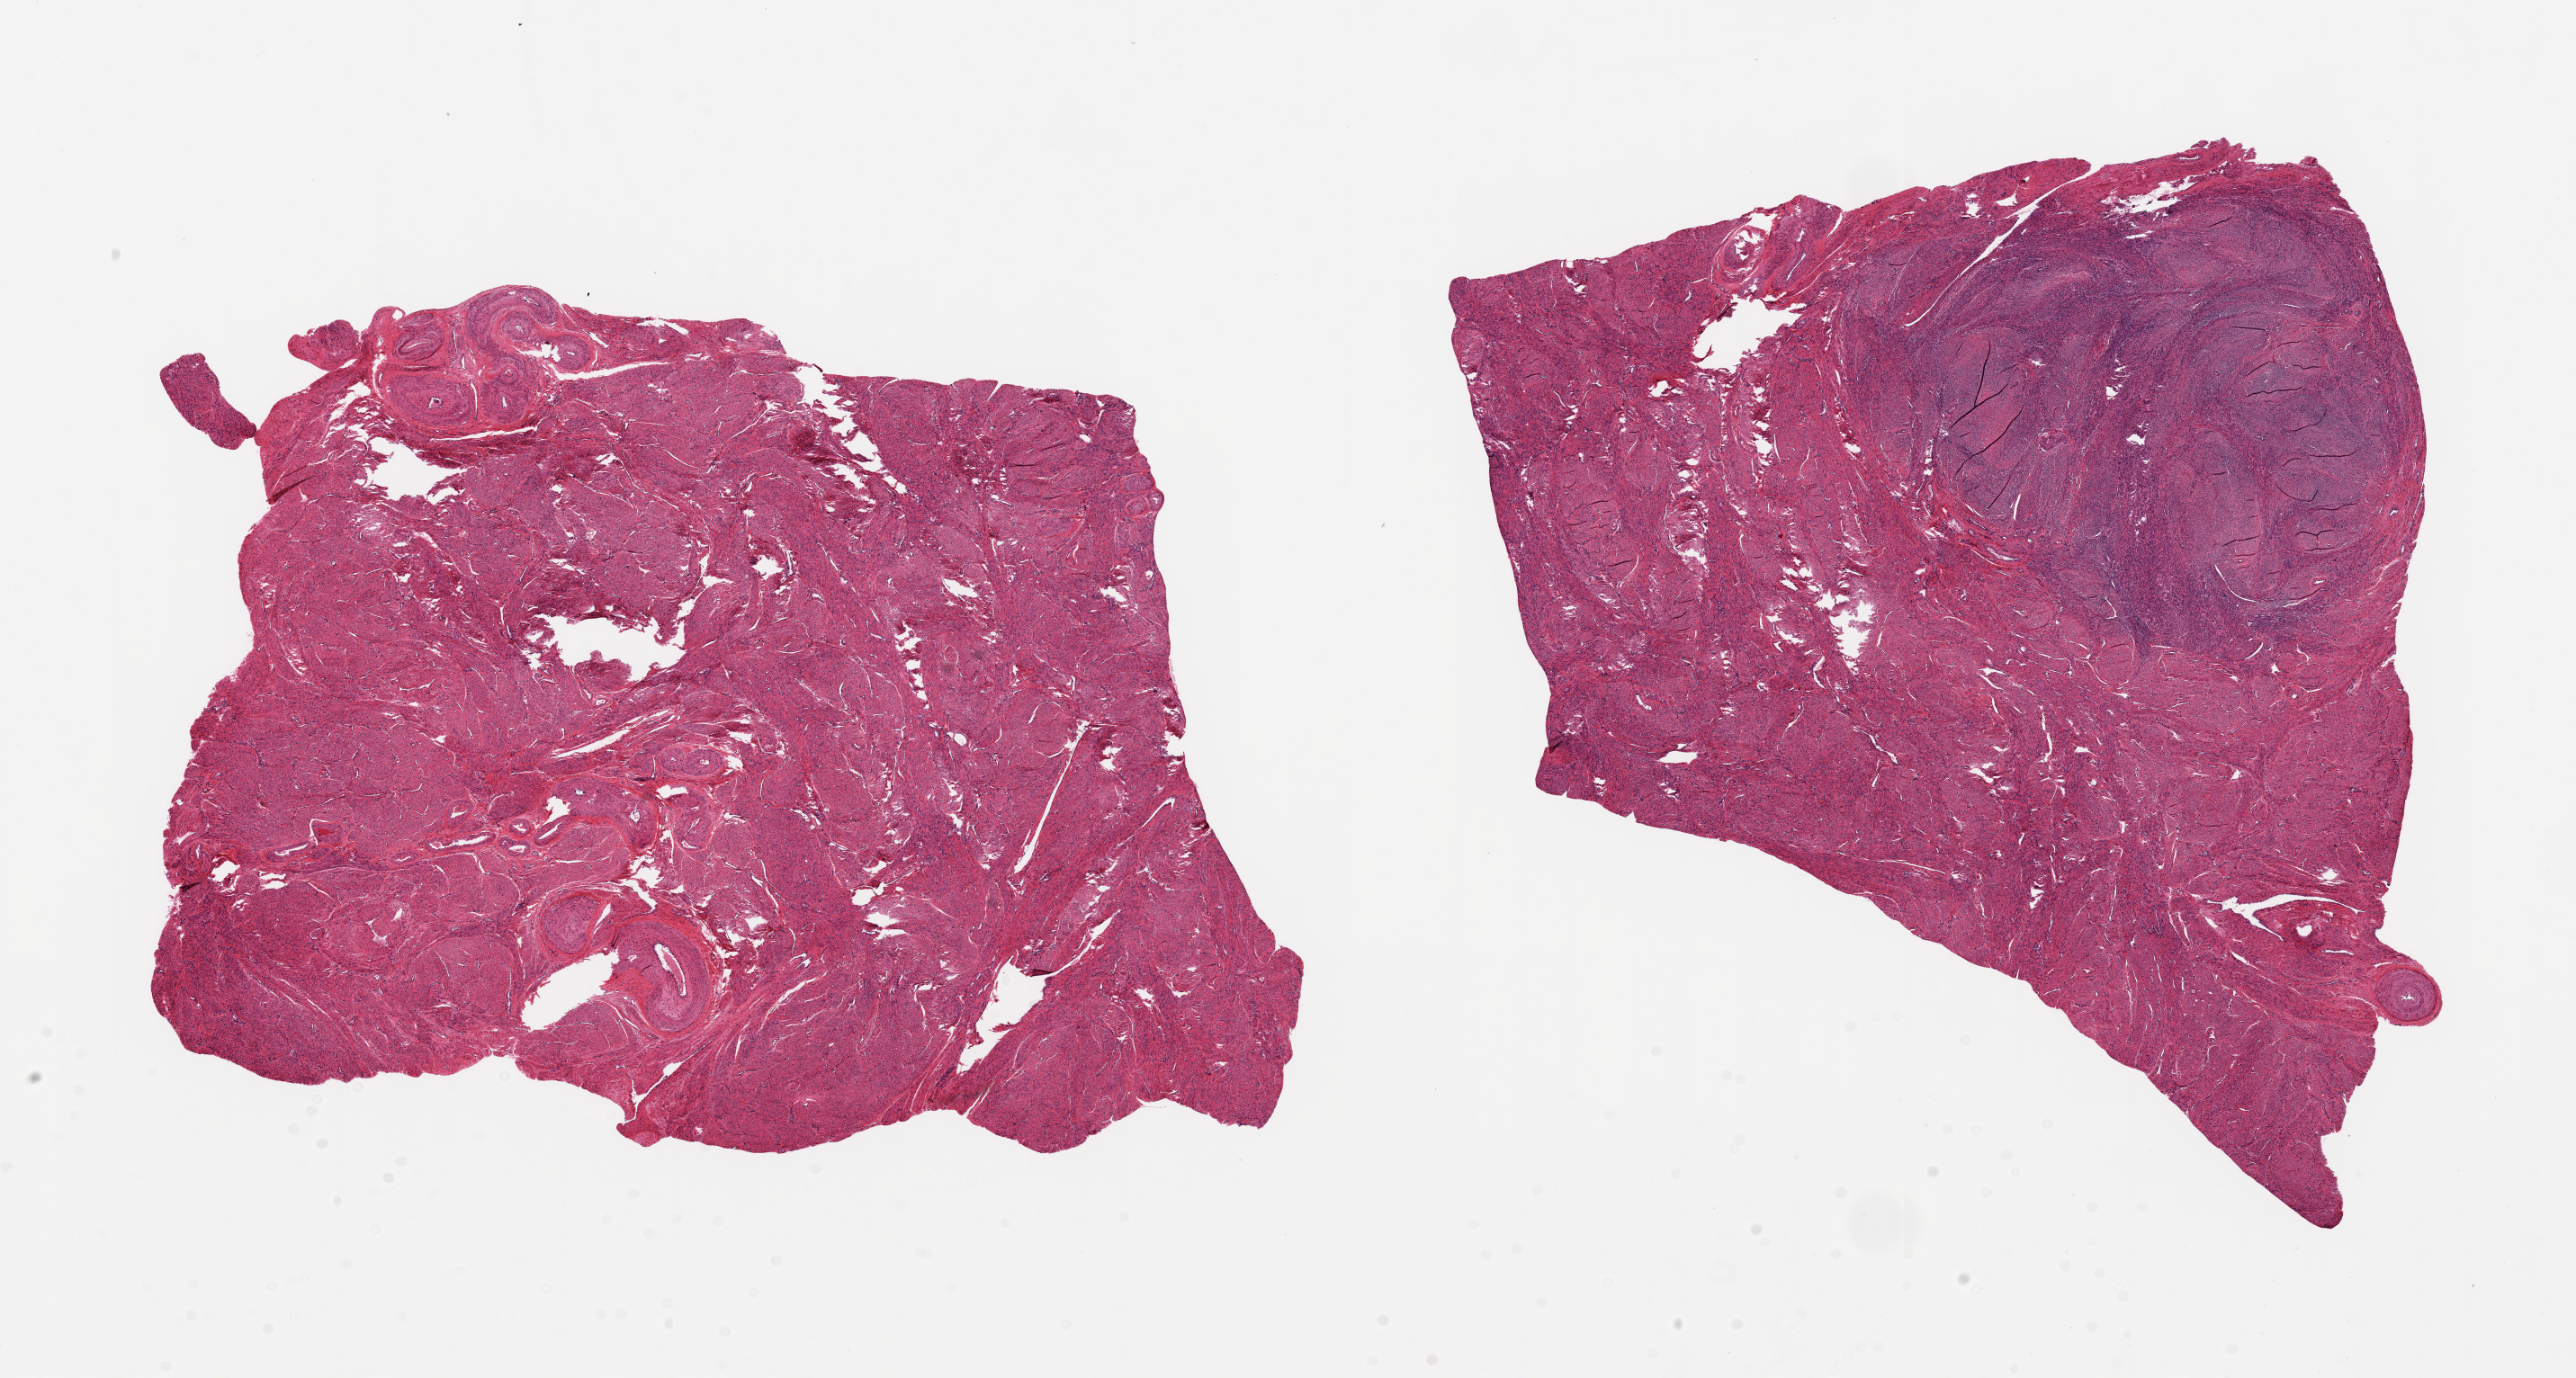
Whole-slide image, haematoxylin and eosin stain, brightfield — a low-resolution overview of the entire scanned area, about 22.6 x 12.1 mm; PAXgene-fixed paraffin-embedded (PFPE) section; section of uterus (target tissue); tissue donor sample. Donor sex: female.
• review note (as recorded): No endometrial glands/ stroma. 2 ~ 6x8mm pieces, one with a 4.6x4mm leiomyoma. Some areas poorly fixed with tears/holes